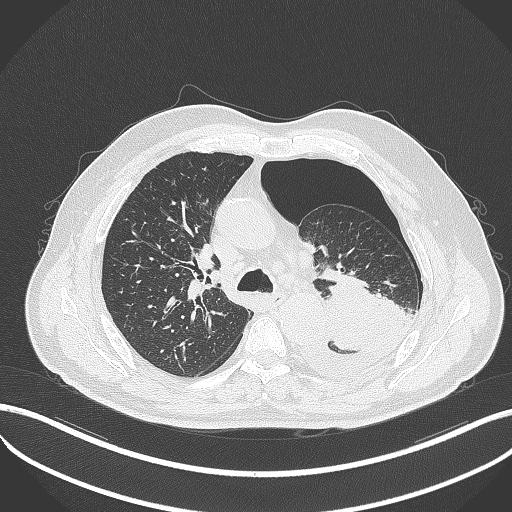
Chest CT, one axial slice; slice 344 of 464 in the series (ordered by position); reconstruction kernel B70f; 120 kVp; lung window (W 1500 / L -600 HU); 1 mm slice thickness; 512 × 512 image matrix, field of view 400 × 400 mm. Patient: male, 76 years. From the clinical record (not read from this slice): clinical TNM (as recorded): T3 N0 M1b.
Annotated regions visible in this slice (bounding box drawn by a radiologist):
- lung tumour (recorded histology: adenocarcinoma): bounding box <324,276,403,353> (left, top, right, bottom; pixels)